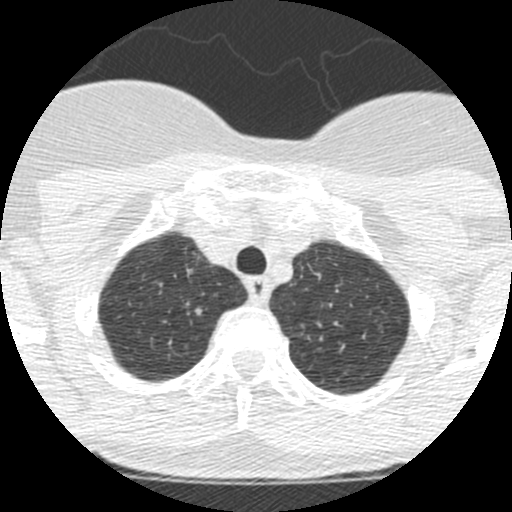
Low-dose screening chest CT, one axial slice; slice 210 of 250 in the series (ordered by position); lung window (W 1500 / L -600 HU); 1.25 mm slice thickness; 512 × 512 image matrix.
Outlined on this slice (manually delineated by an expert):
- lesion 1 (tumor, upper lobe of right lung): bounding box [x1, y1, x2, y2] px = [195, 308, 202, 315]